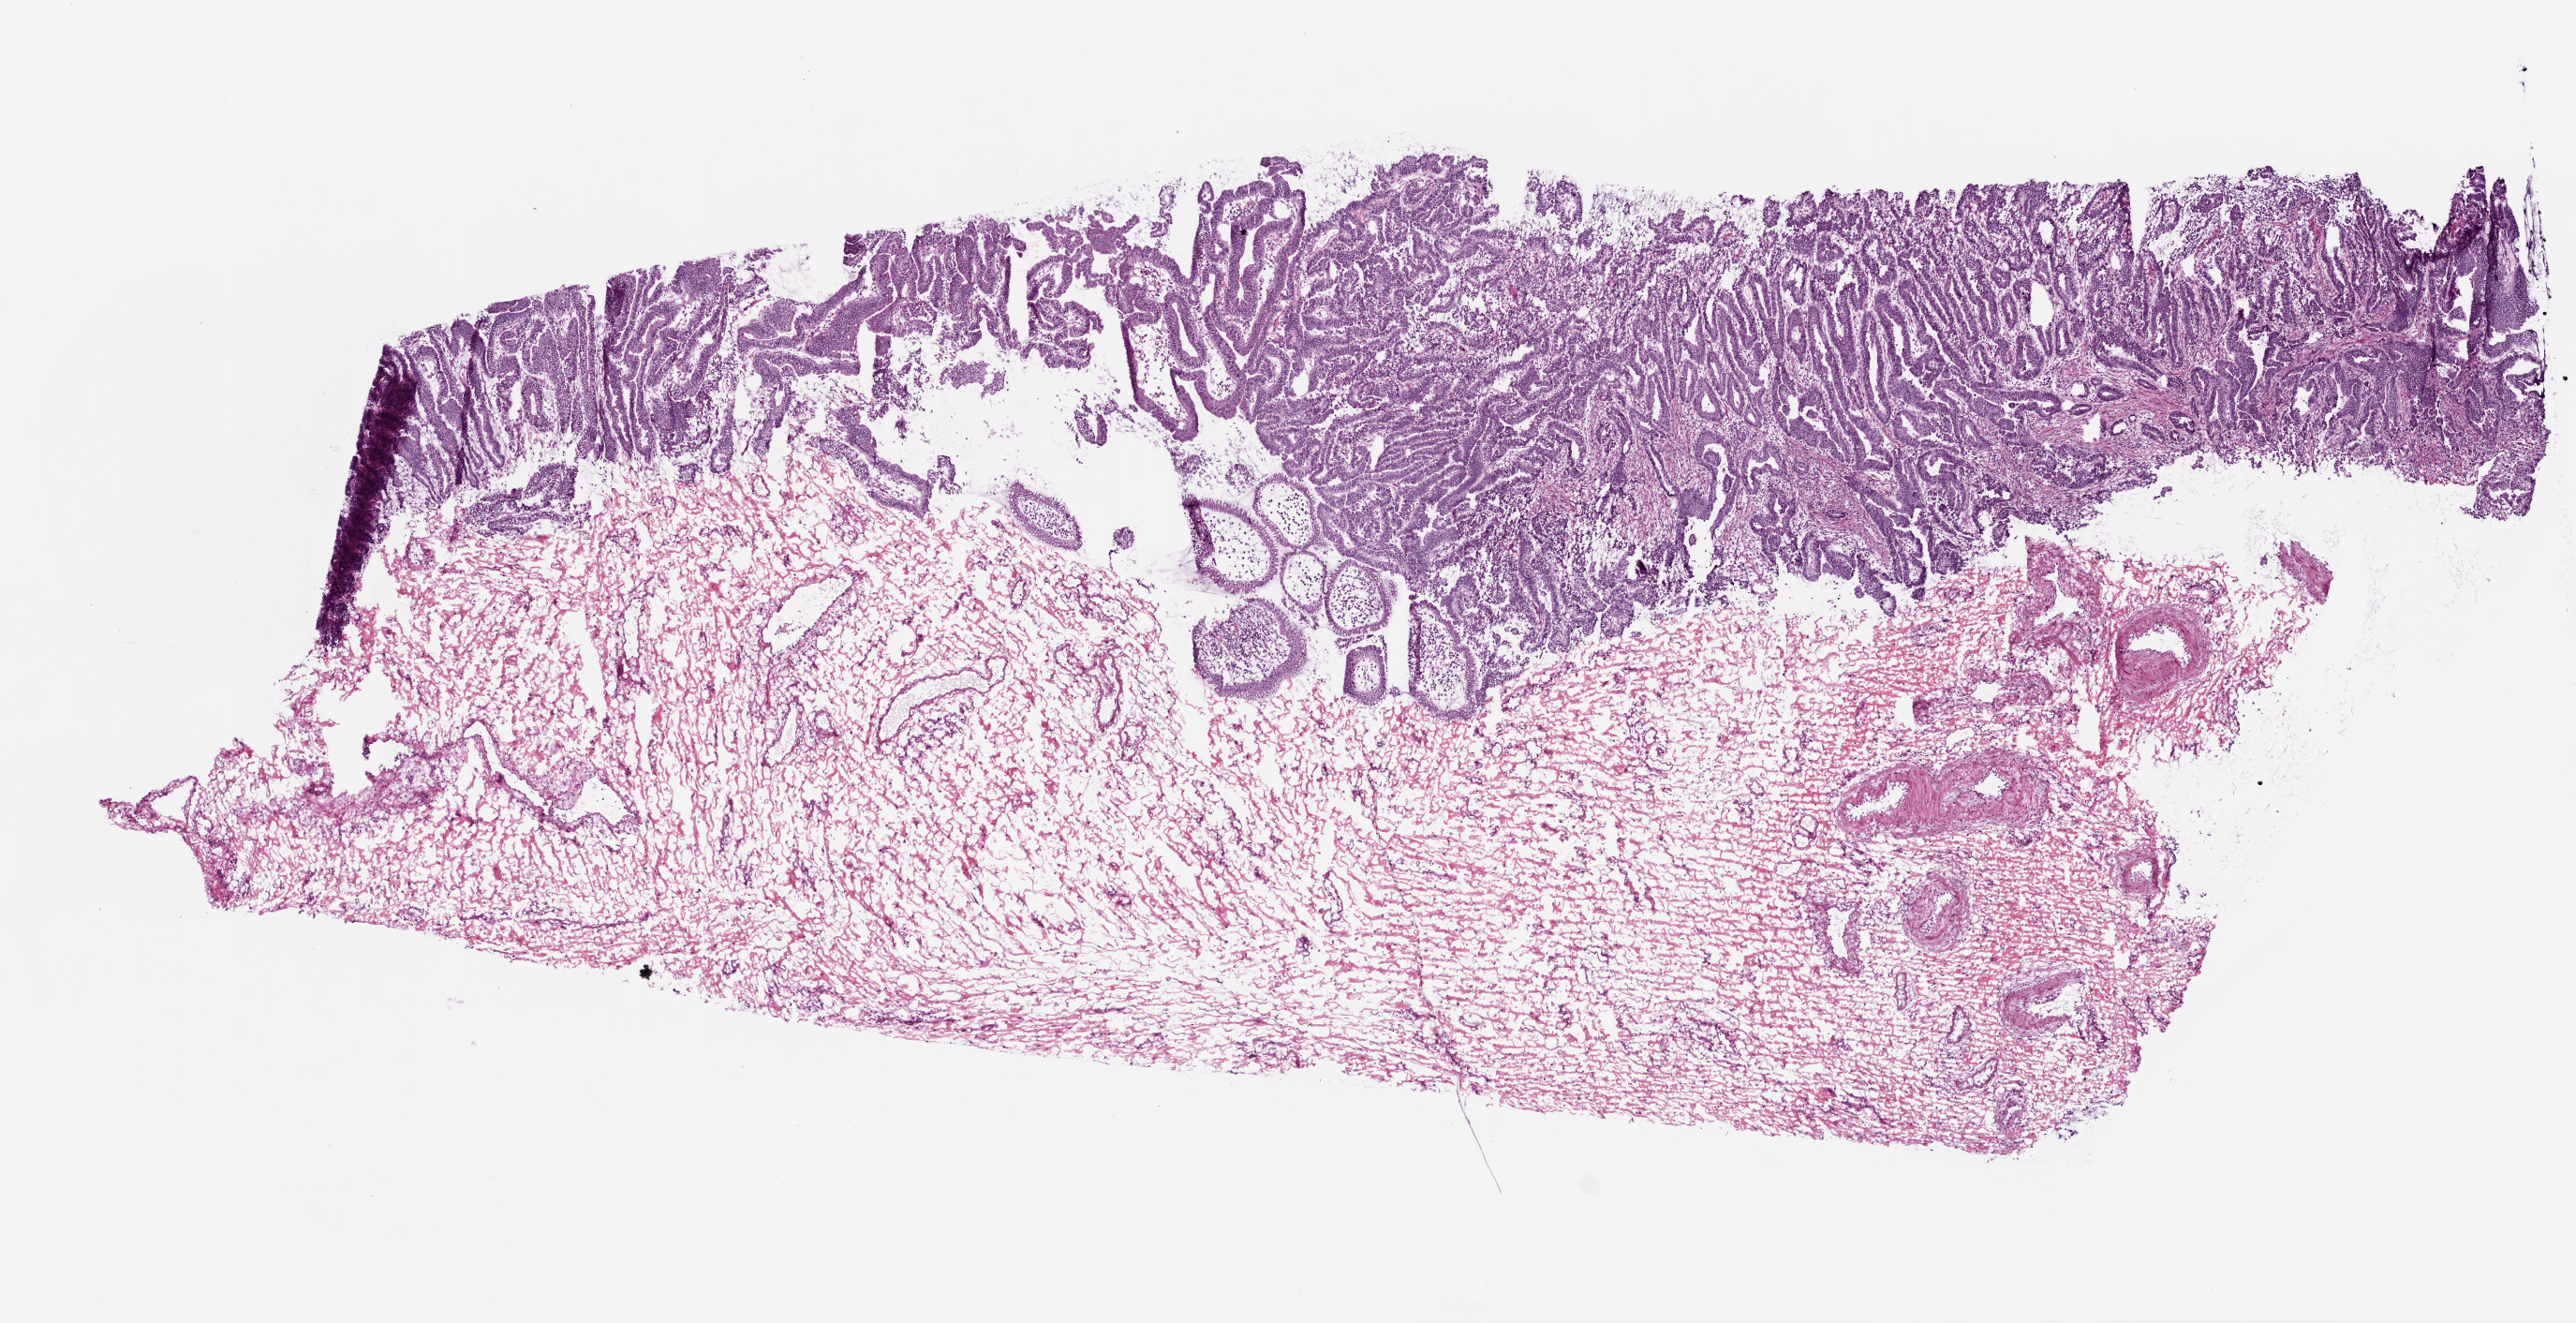
Digitized H&E-stained tissue section (whole slide), shown as a low-resolution overview of the whole scanned area (about 11.0 x 5.7 mm, acquisition: 20x scan). Frozen section from the top of the tissue portion. Stomach, primary tumour sample. Male, age 73 years at initial diagnosis. Histologic grade: G2 (moderately differentiated). Pathologist review of this section (percent, as recorded): tumour cells 30%, tumour nuclei 75%, normal cells 10%, stromal cells 55%, necrosis 5%.
• AJCC pathologic stage: IA (5th edition)
• diagnosis: Adenocarcinoma, intestinal type (gastric antrum)
• TNM: T1 N0 M0